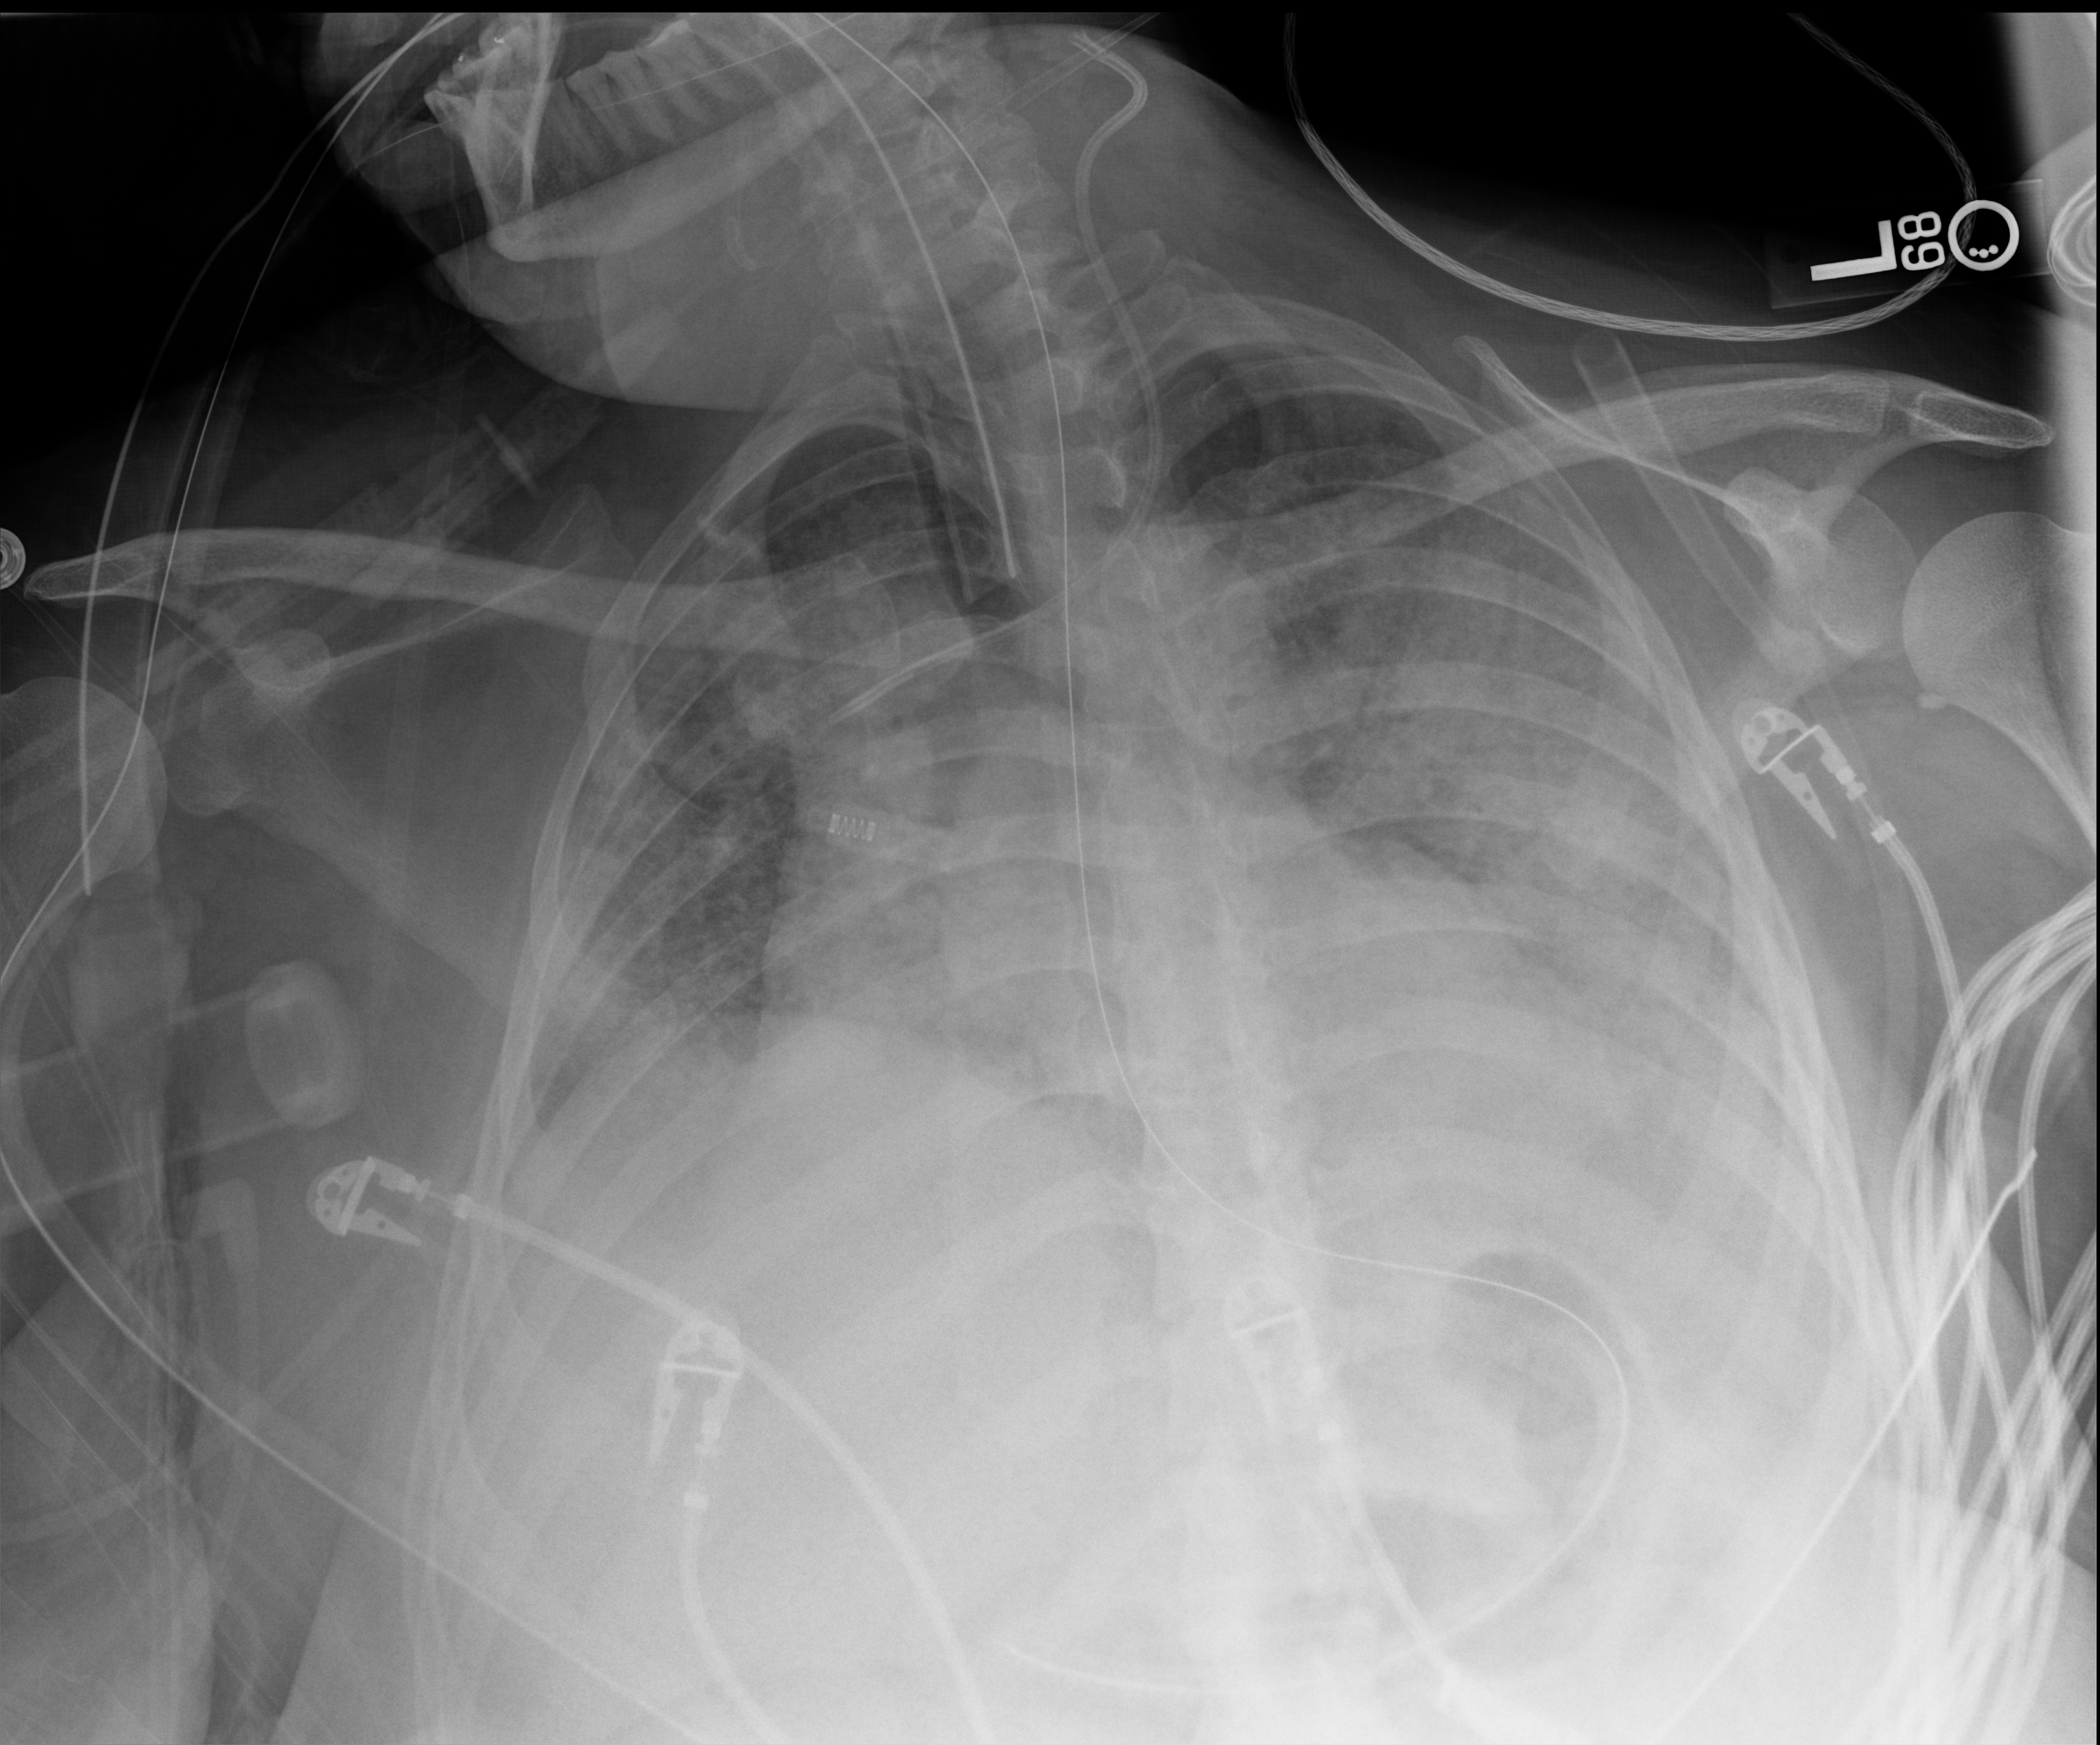
Chest radiograph, anteroposterior (AP) projection. Female patient hospitalised with COVID-19, age 18–59 years.
Admission-level facts for this patient (not findings on this image; timing relative to this image not recorded): admitted to intensive care during this hospital stay: no.